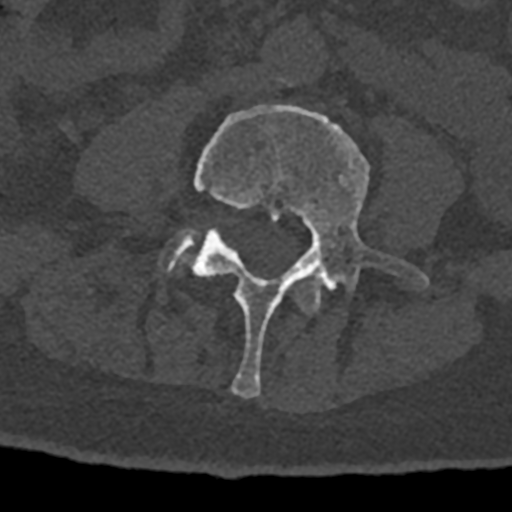
CT including the spine, one axial slice. Position 259 of 797 along the scan axis. Reconstruction kernel Br40s/3. Bone window (W 1800 / L 400 HU). 0.5 mm slice thickness. 512 × 512 image matrix, field of view 160 × 160 mm. Patient: male, 74 years. From the clinical record (not read from this slice): primary cancer: renal; vertebrae with lytic lesions (as recorded): T10, L1, L2, L3, L4, L5.
Outlined on this slice (semi-automatically segmented with operator editing):
- L3 vertebra: bounding box [x1, y1, x2, y2] px = [295, 274, 323, 313]
- L4 vertebra: [190, 105, 429, 397]
- L5 vertebra: [162, 229, 195, 271]